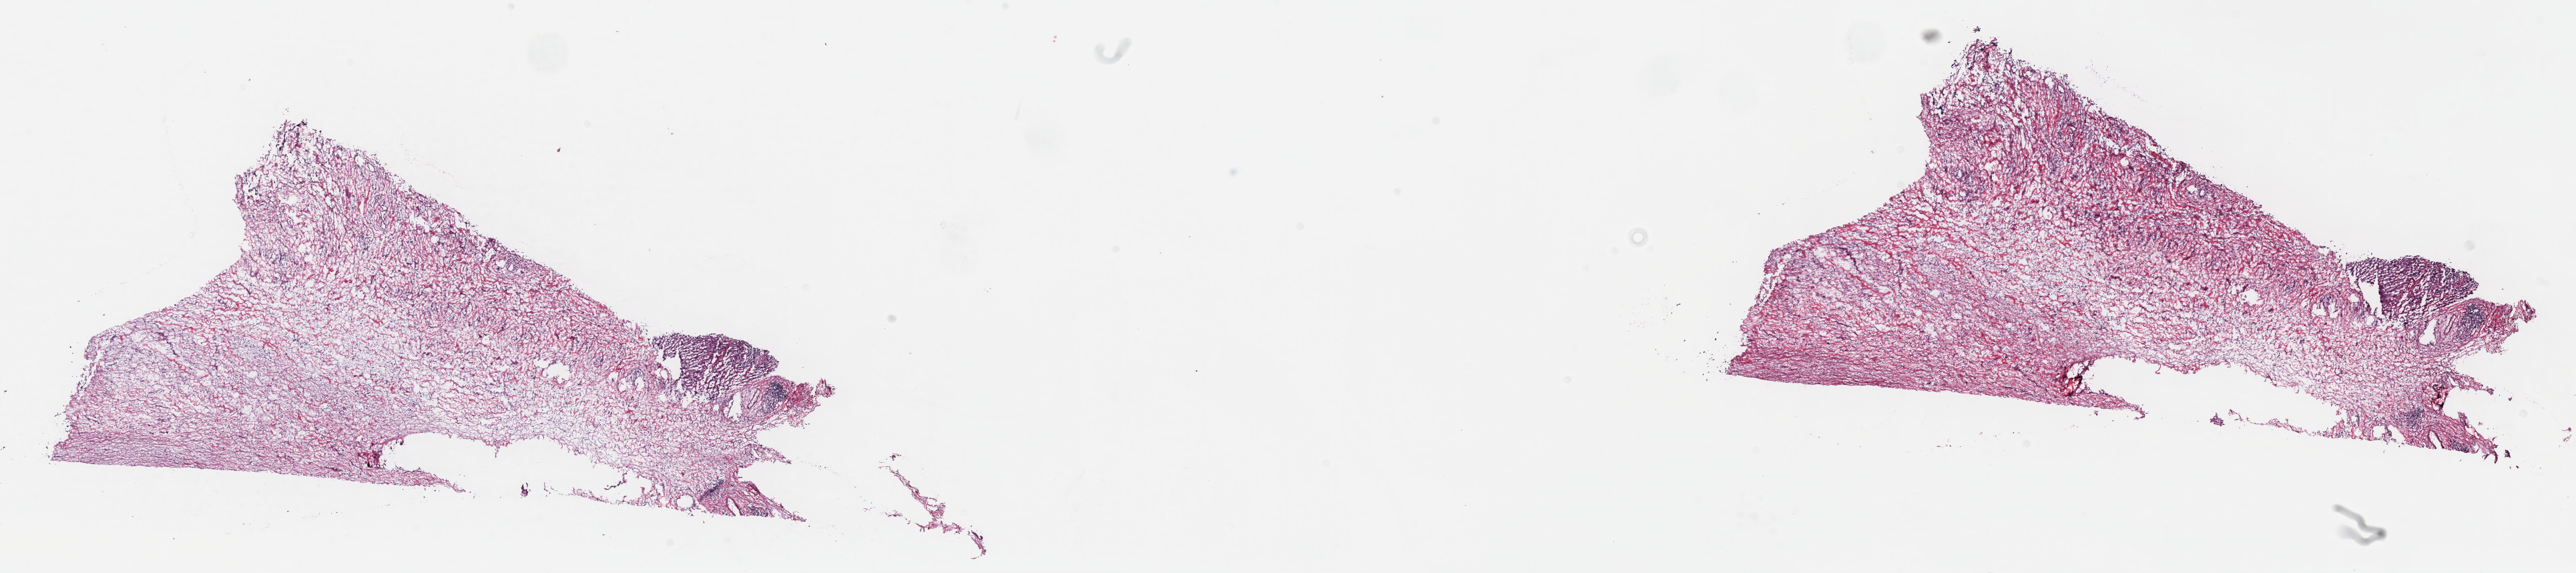
H&E whole-slide image — low-resolution overview of the scanned area, about 31.2 x 6.9 mm (from a 40x scan). Frozen section. Bladder, primary tumour sample. Patient: female, age at initial diagnosis 74 years. Histologic grade: high grade. Composition of this section per pathologist review: tumour cells 15%, tumour nuclei 85%, normal cells 0%, stromal cells 75%, necrosis 10%. Inflammatory infiltration, as recorded: lymphocyte infiltration 10%, monocyte infiltration 0%, neutrophil infiltration 3%.
Diagnosis: Transitional cell carcinoma. TNM: T3b N0 MX. AJCC pathologic stage: III (6th edition).